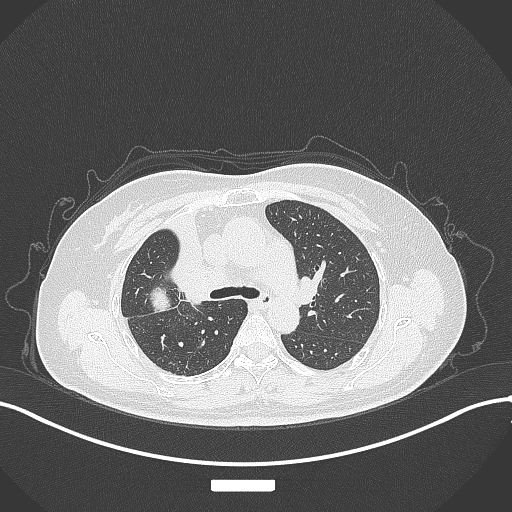
Chest CT, one axial slice; slice 206 of 309 in the series (ordered by position); reconstruction kernel B70f; 120 kVp; lung window (W 1500 / L -600 HU); 1 mm slice thickness; 512 × 512 image matrix, field of view 400 × 400 mm. Patient: female, 60 years. Case-level facts recorded for this patient, not image findings: clinical TNM (as recorded): T3 N1 M1.
Annotated regions visible in this slice (bounding box drawn by a radiologist):
- lung tumour (recorded histology: adenocarcinoma): bounding box <142,276,183,324> (left, top, right, bottom; pixels)